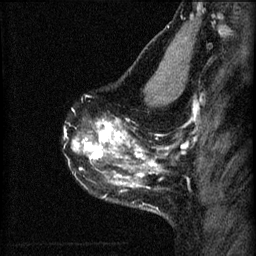
Breast MRI (dynamic contrast-enhanced), one sagittal slice; position 44 of 60 along the scan axis; 3 images stored at this slice position (order not interpretable as contrast timing); 1.5 T; TE 4.2 ms, TR 8.2 ms; 2 mm slice thickness; 256 × 256 image matrix, field of view 180 × 180 mm. Patient: female, 40 years.
Annotated regions visible in this slice (semi-automatically segmented with operator editing):
- analysis volume of interest (the breast-tissue region the enhancement analysis was run in; not a lesion): bounding box <66,76,179,219> (left, top, right, bottom; pixels)
- tumour enhancement mask (voxels above the 70 % enhancement threshold inside the analysis volume of interest): <66,120,161,187>